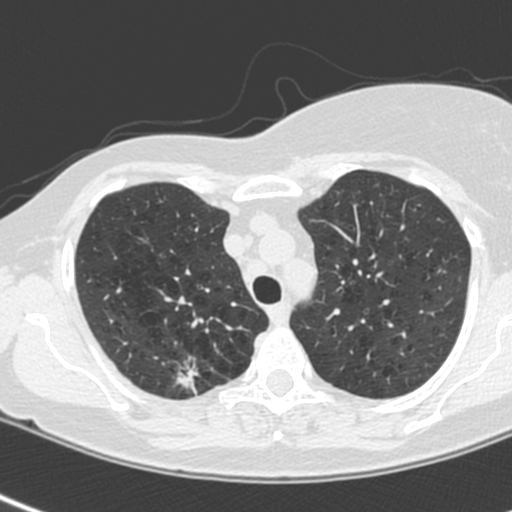
Chest CT (low-dose screening protocol), one axial image. Baseline screening round. Lung window (W 1500 / L -600 HU). 120 kVp. Slice 42 of 214 in the series. Female participant, aged 64 years at enrolment. Current smoker at enrolment.
Lesion marked by an expert reader, bounding box [x1, y1, x2, y2] px = [165, 355, 221, 405]. The exam's reader record, not a measurement of the box and not confirmed to be the same lesion: non-calcified nodule or mass ≥4 mm, right upper lobe, 13 × 10 mm, spiculated (stellate) margins, soft tissue attenuation. Participant outcome: lung cancer diagnosed 21 days after this screen — adenocarcinoma, NOS, right upper lobe, poorly differentiated (G3), stage IIIB (AJCC 6th edition), 20 mm at pathology.